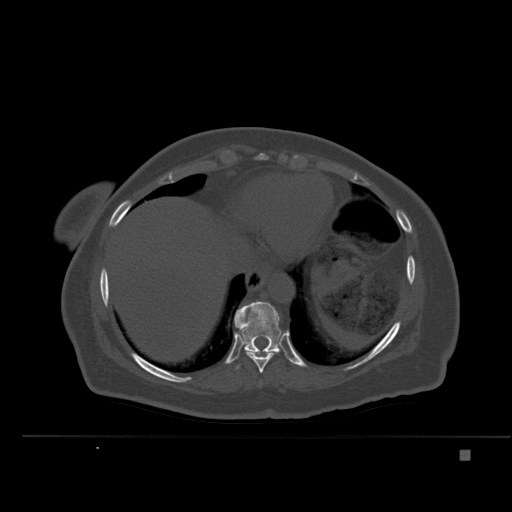
CT including the spine, one axial slice; position 290 of 477 along the scan axis; bone window (W 1800 / L 400 HU); 512 × 512 image matrix. Female patient, age 74 years. Case-level facts recorded for this patient, not image findings: primary cancer: colon.
Structures marked on this image (semi-automatically segmented with operator editing):
- T10 vertebra: box from (x=234, y=301) to (x=282, y=353) px
- T9 vertebra: (x=236, y=326)–(x=278, y=373)